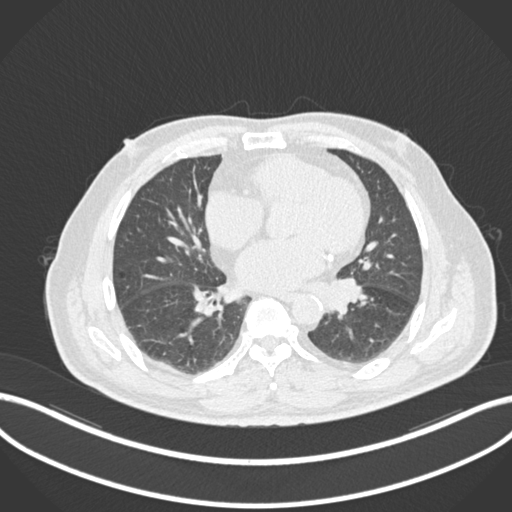
Chest CT, one axial slice; position 55 of 161 along the scan axis; lung window (W 1500 / L -600 HU); 1 mm slice thickness; 512 × 512 image matrix. Patient: male, 71 years. From the clinical record (not read from this slice): clinical TNM (as recorded): T1b N0 M0.
Outlined on this slice (rectangle marked by the reading radiologist):
- lung tumour (recorded histology: squamous cell carcinoma): bounding box <321,276,364,315> (left, top, right, bottom; pixels)